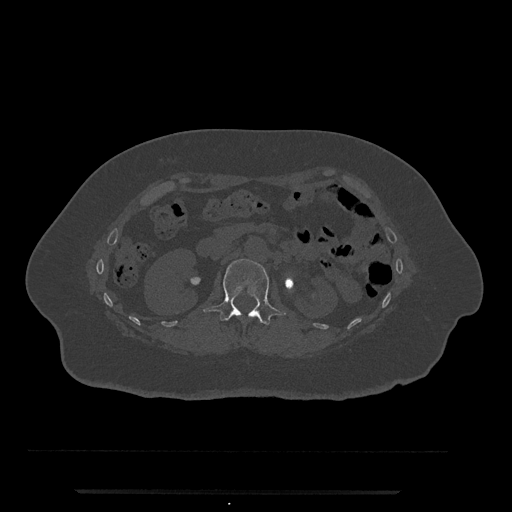
CT including the spine, one axial slice. Slice 107 of 797 in the series (ordered by position). Bone window (W 1800 / L 400 HU). 0.5 mm slice thickness. 512 × 512 image matrix. Female patient, age 51 years. From the clinical record (not read from this slice): primary cancer: neuro; vertebrae with lytic lesions (as recorded): T8.
Structures marked on this image (semi-automatic segmentation, software-assisted and operator-edited):
- L1 vertebra: bounding box (x1, y1, x2, y2) in pixels: (203, 259, 286, 325)